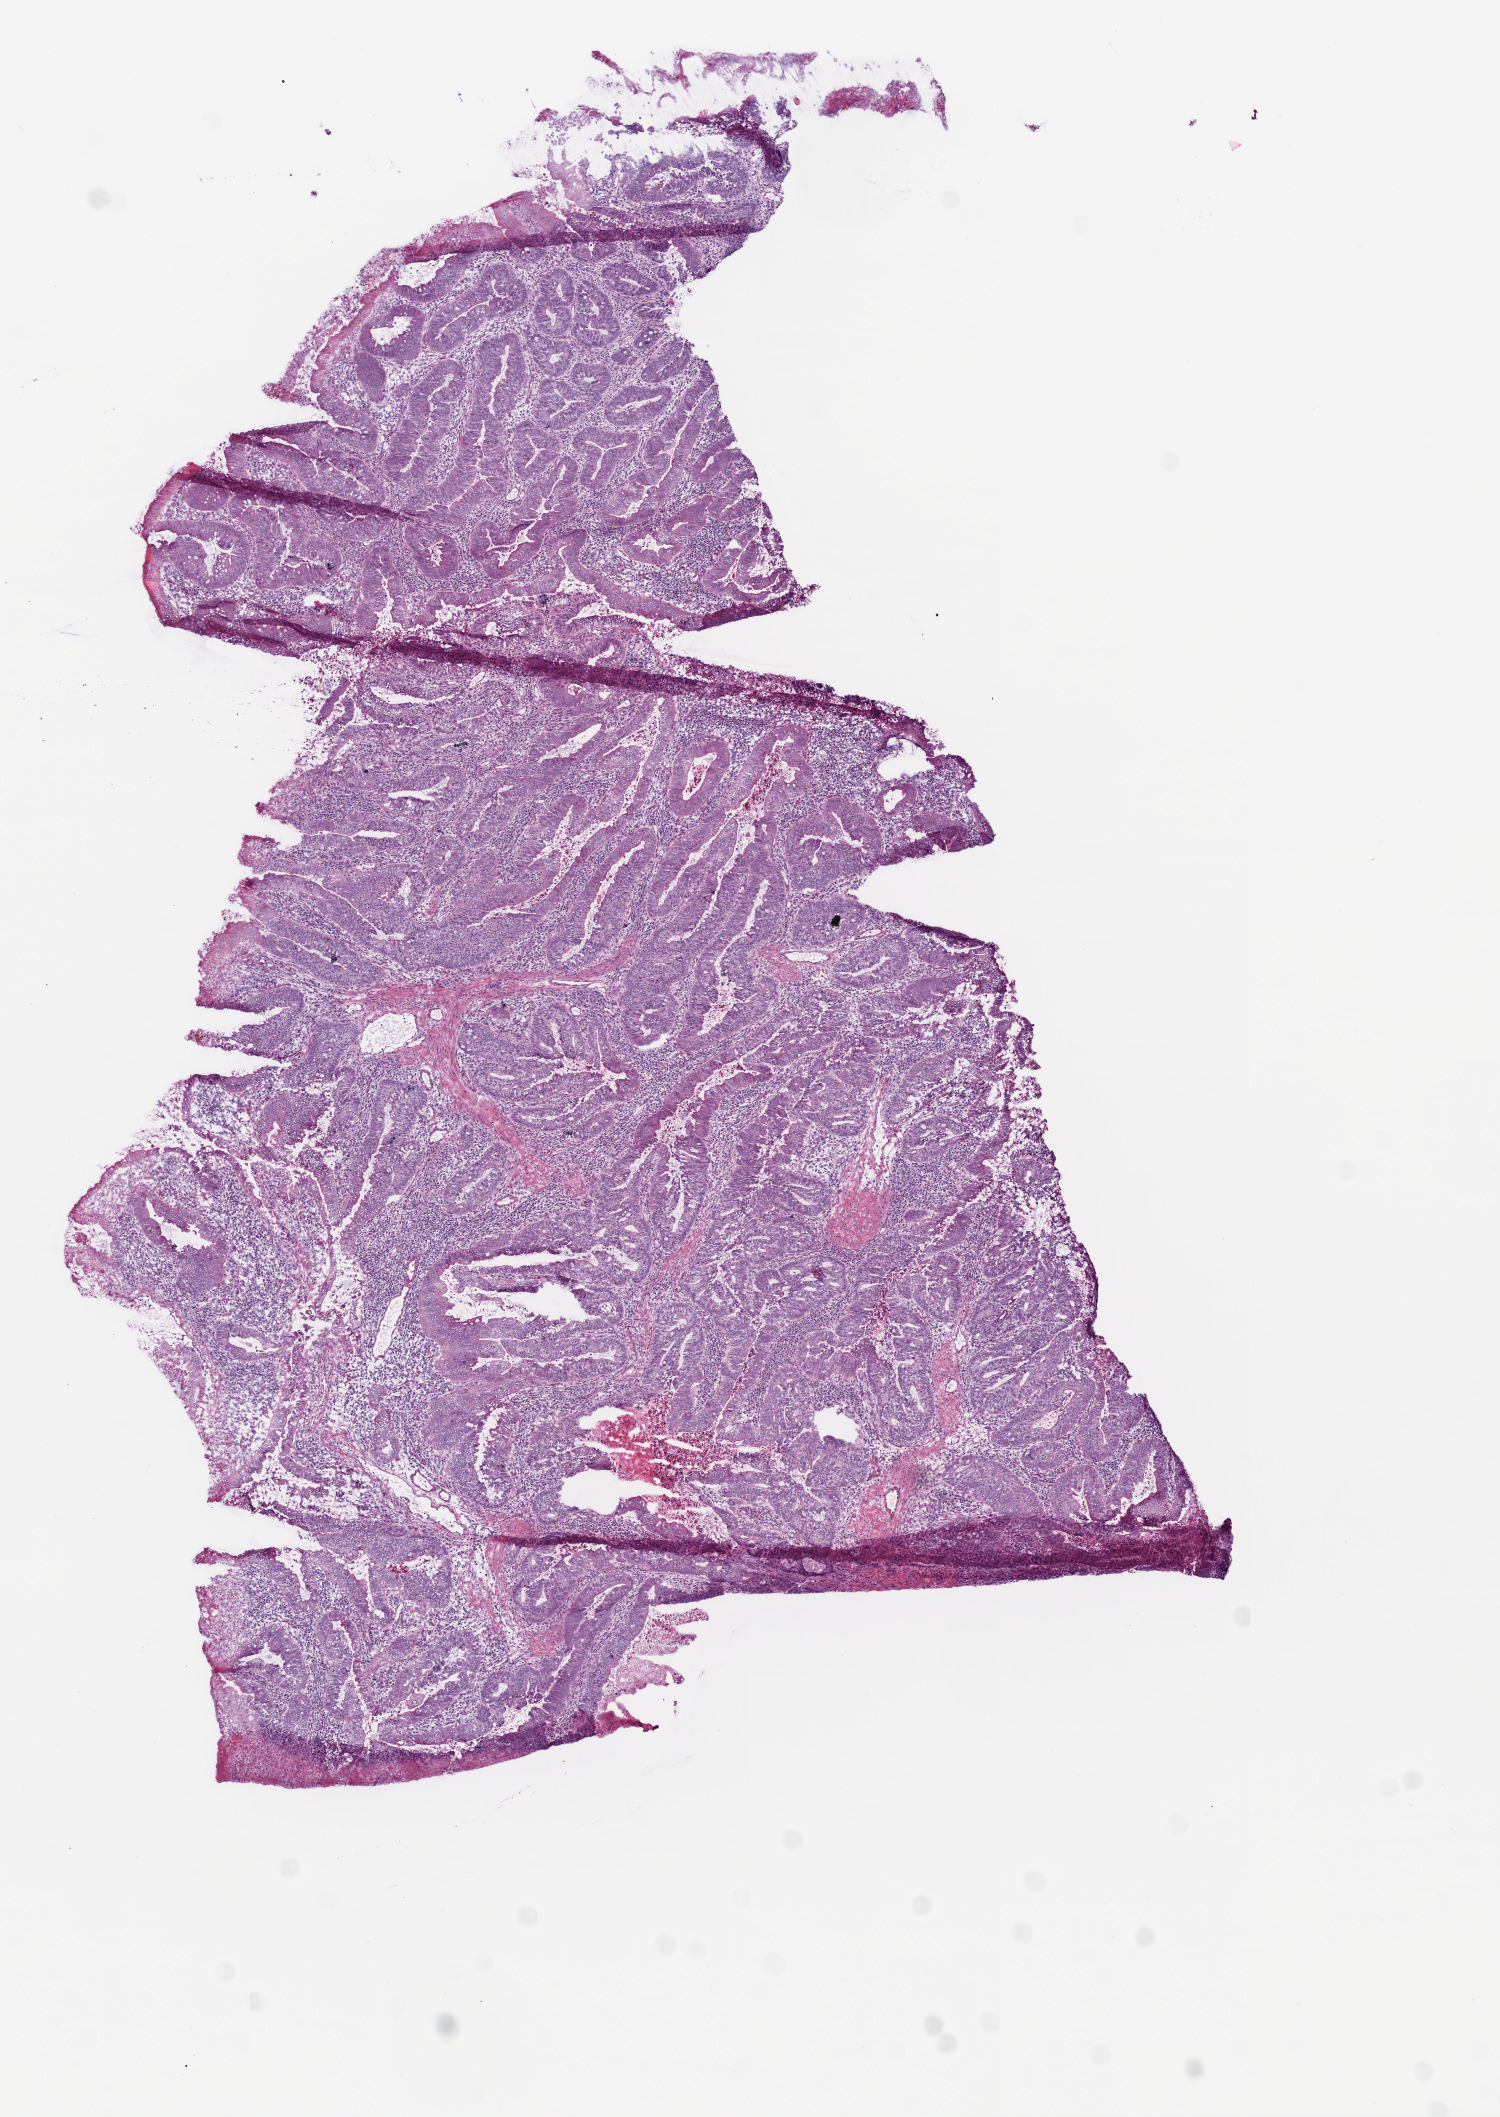
Digitized H&E tissue section (whole slide) — whole scanned area (about 6.0 x 8.5 mm) shown as a low-resolution overview, frozen section from the top of the tissue portion, colon, primary tumour sample. Male patient; age at initial diagnosis 66 years. Pathologist review of this section (percent, as recorded): tumour cells 80%, tumour nuclei 85%, normal cells 0%, stromal cells 10%, necrosis 10%.
* lymph nodes positive (case pathology): 0 of 12 examined
* AJCC pathologic stage: IIA (6th edition)
* histologic diagnosis: Adenocarcinoma, NOS
* TNM: T3 N0 M0